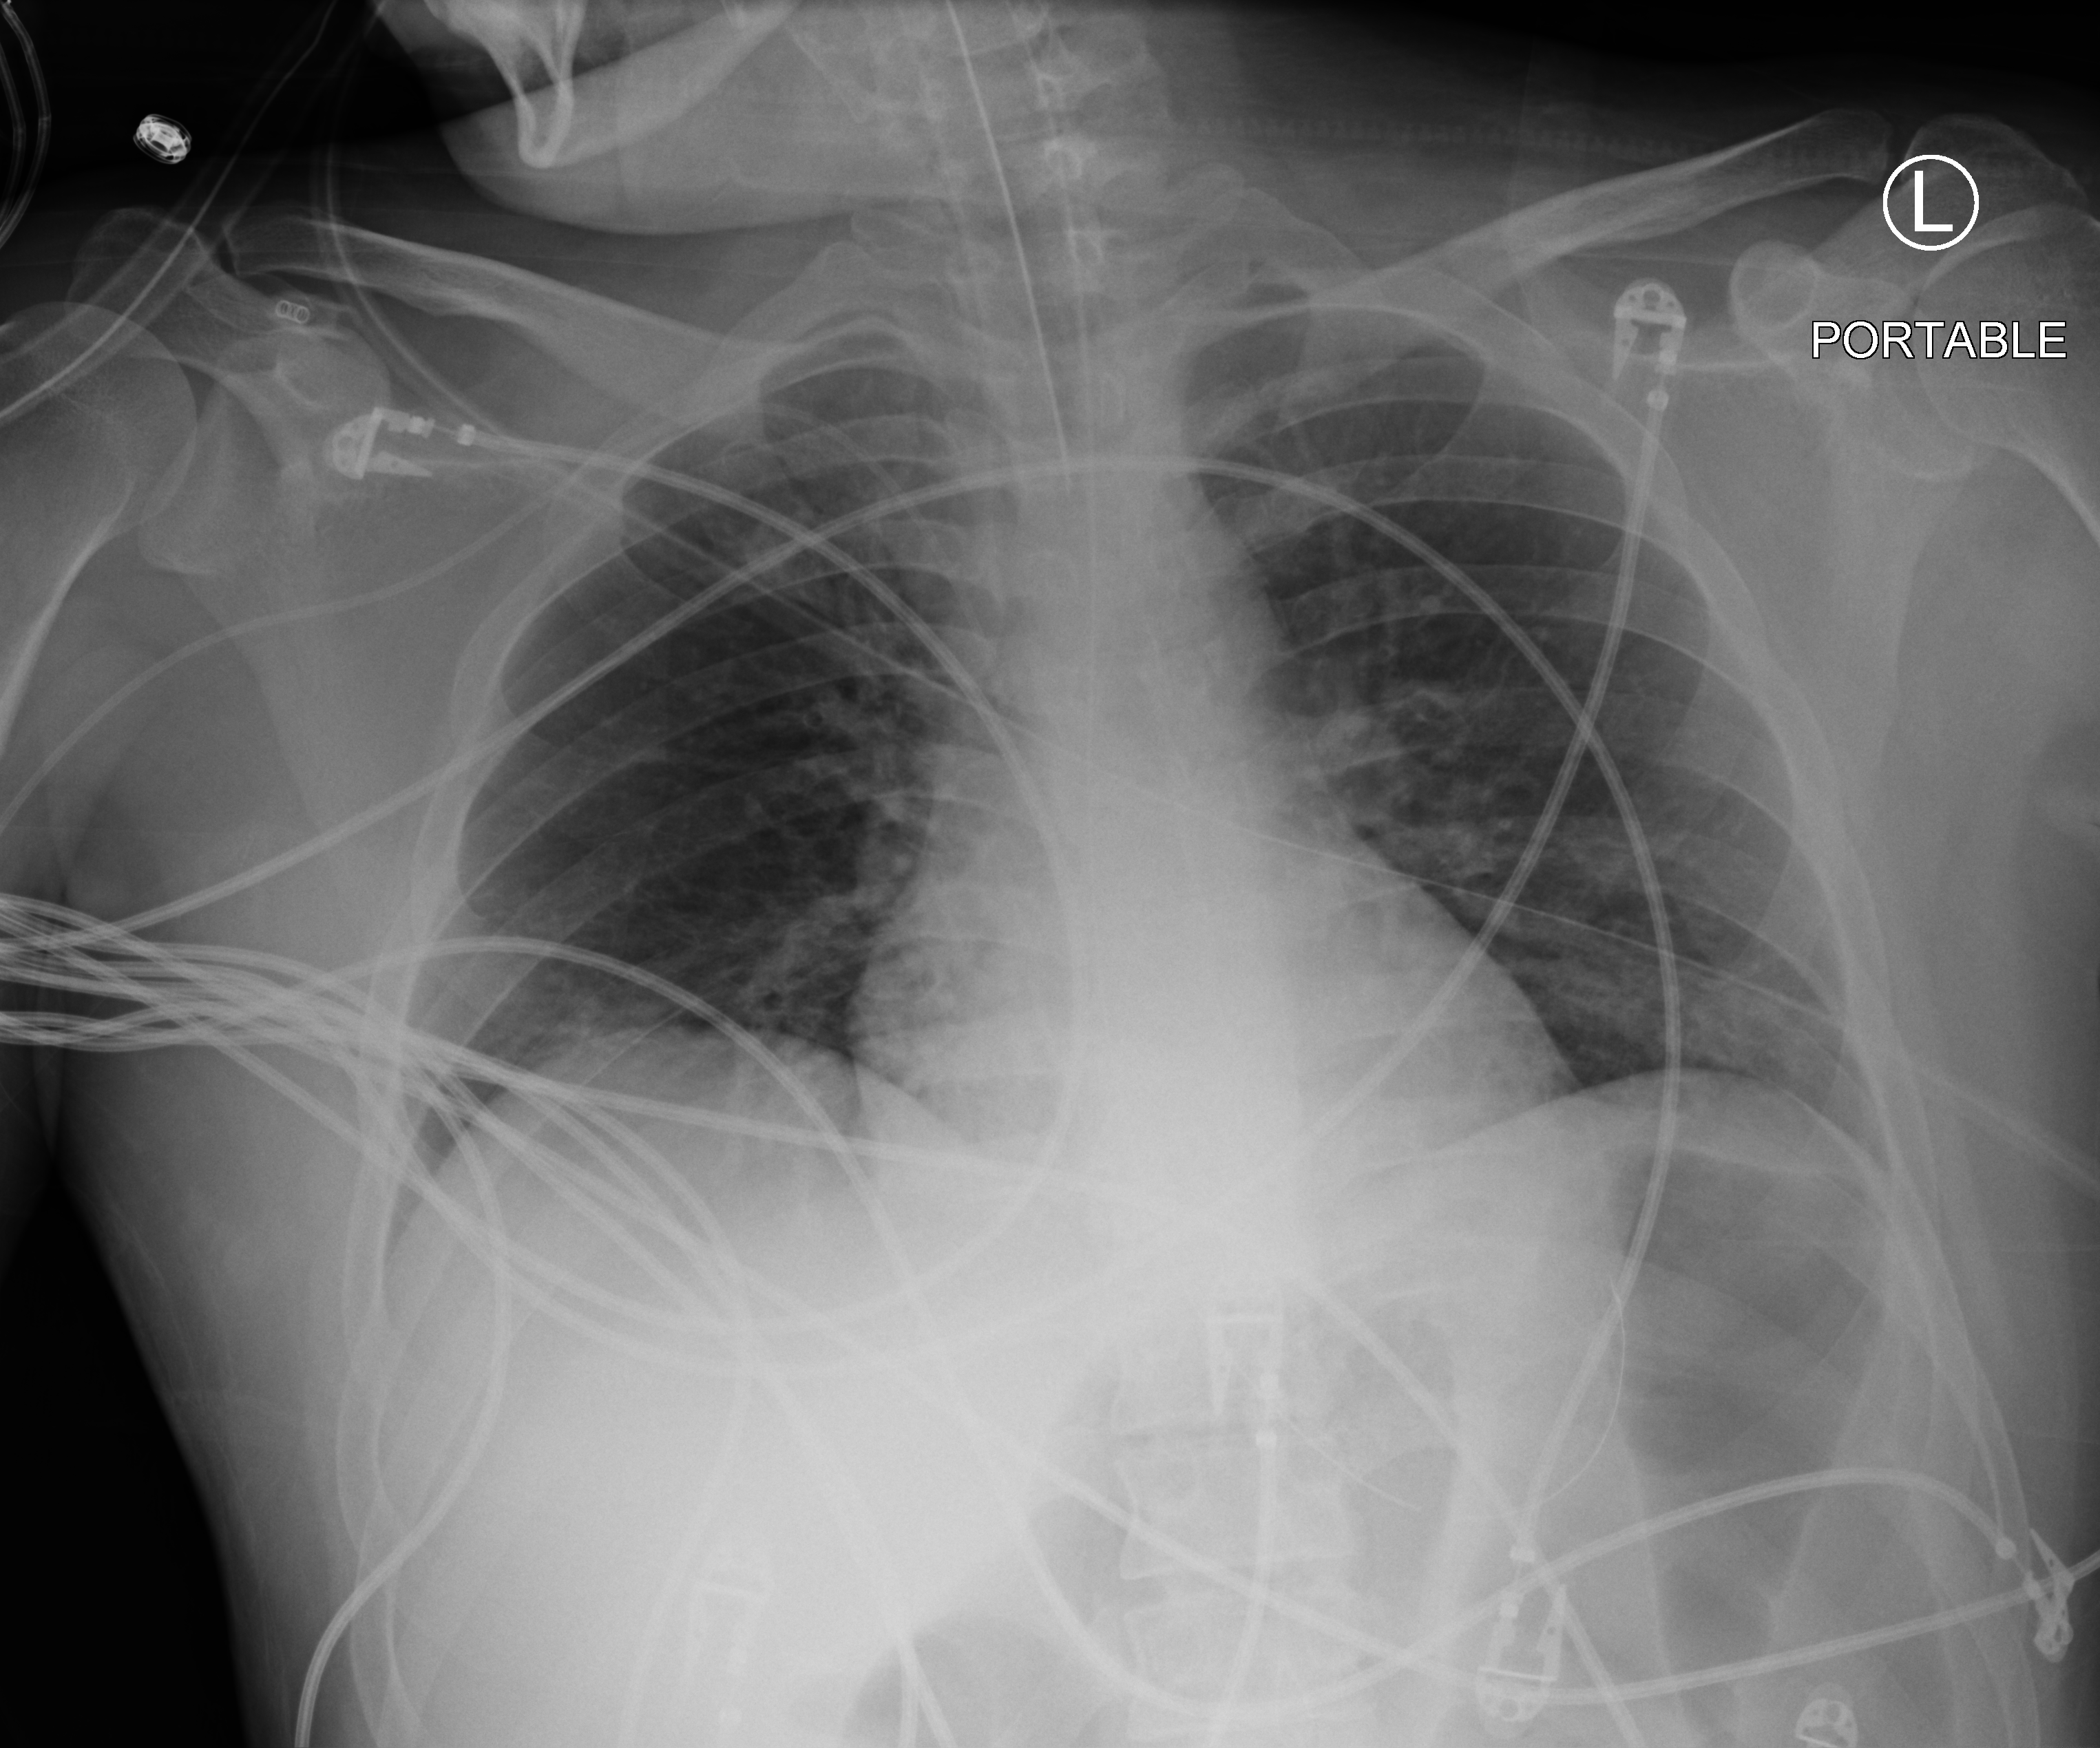
Chest X-ray (portable); anteroposterior (AP) projection. Male patient hospitalised with COVID-19, age 18–59 years.
Admission-level facts for this patient (not findings on this image; timing relative to this image not recorded): COPD (admission record): no; admitted to intensive care during this hospital stay: yes; chronic kidney disease (admission record): no.